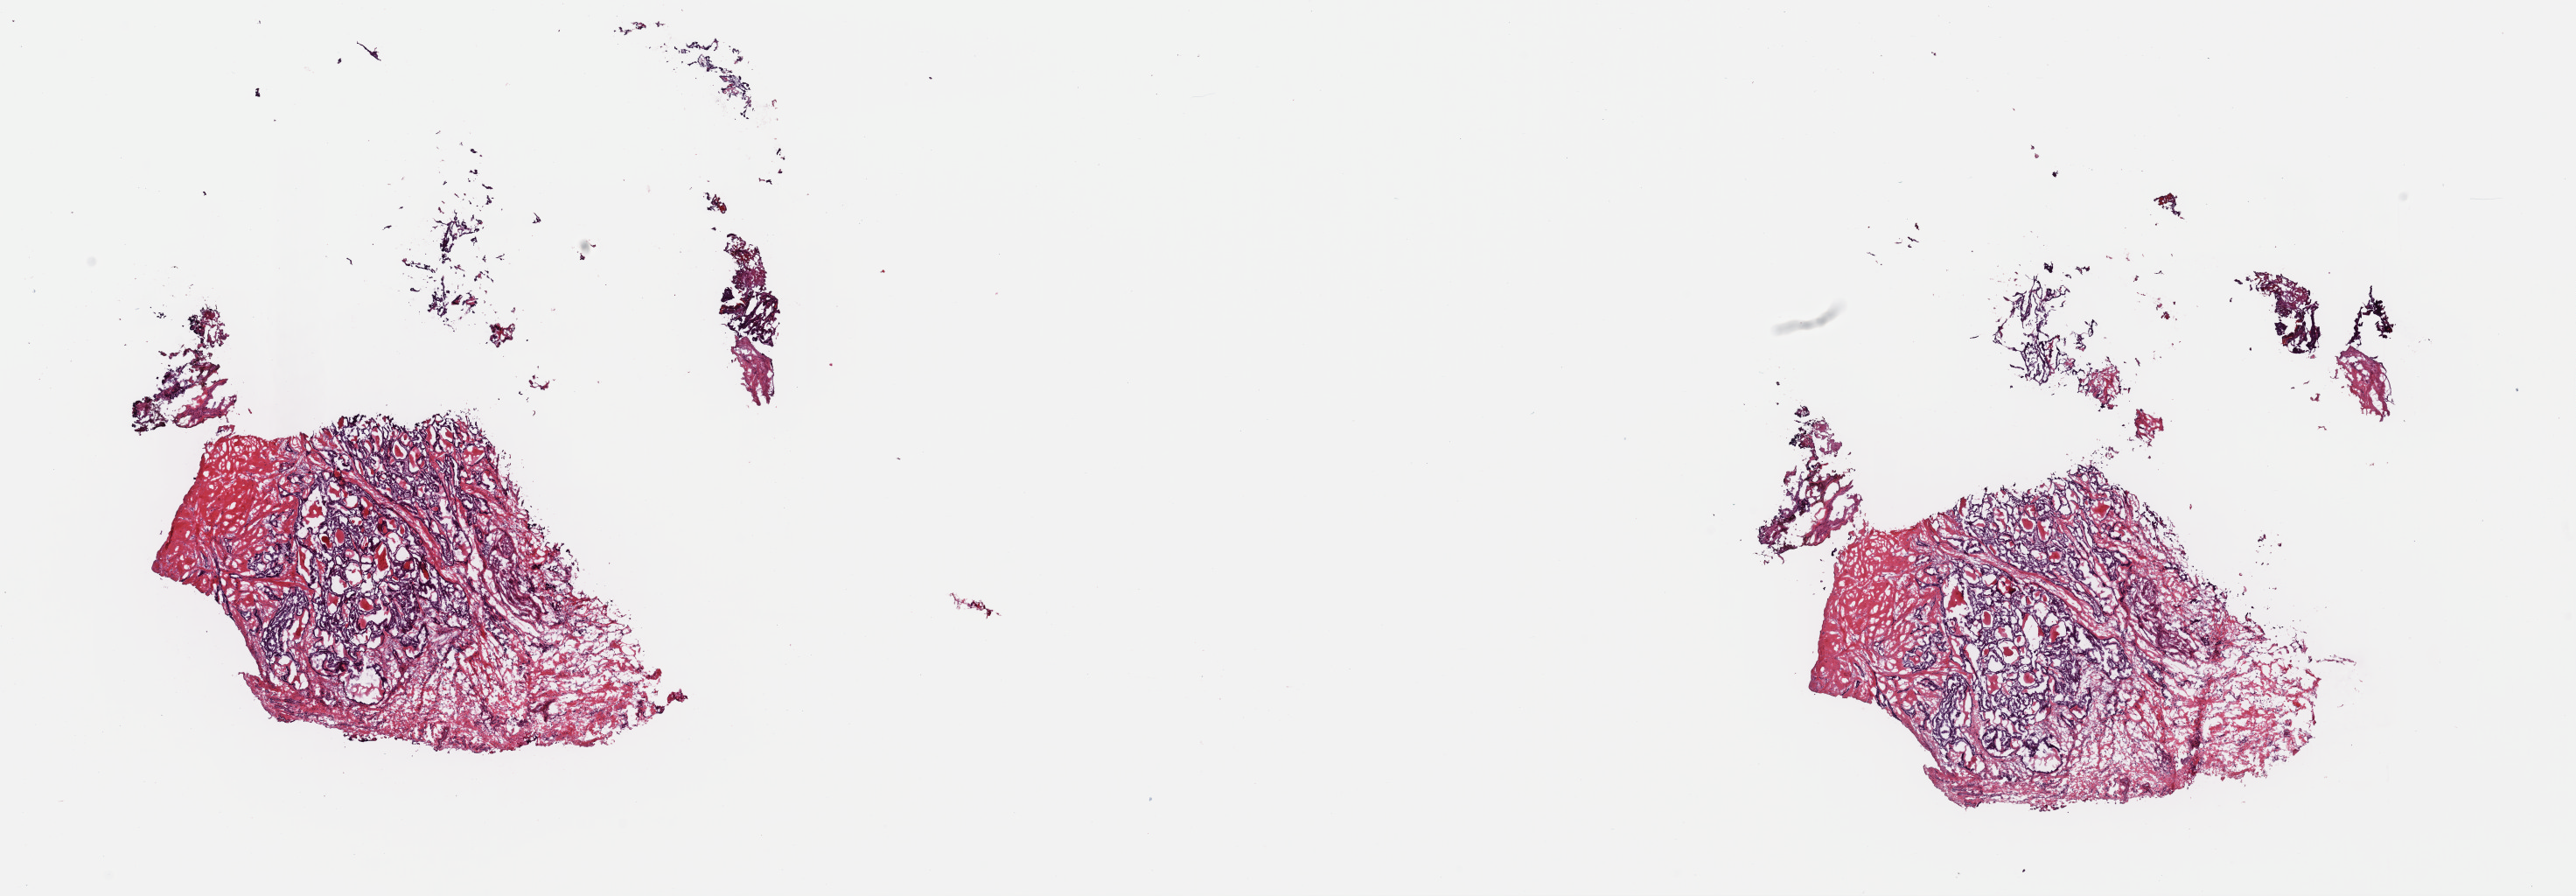
H&E whole-slide image, a low-resolution overview of the entire scanned area, about 23.3 x 8.1 mm, frozen section from the top of the tissue portion, primary tumour sample from the thyroid. Patient: female, age at initial diagnosis 64 years. Composition of this section per pathologist review: tumour cells 75%, tumour nuclei 85%, normal cells 0%, stromal cells 25%, necrosis 0%. Inflammatory infiltration, as recorded: lymphocyte infiltration 0%, monocyte infiltration 0%, neutrophil infiltration 0%.
• diagnosis: Papillary adenocarcinoma, NOS (thyroid gland)
• AJCC pathologic stage: III (4th edition)
• laterality: bilateral
• lymph nodes positive (case pathology): 3 of 16 examined